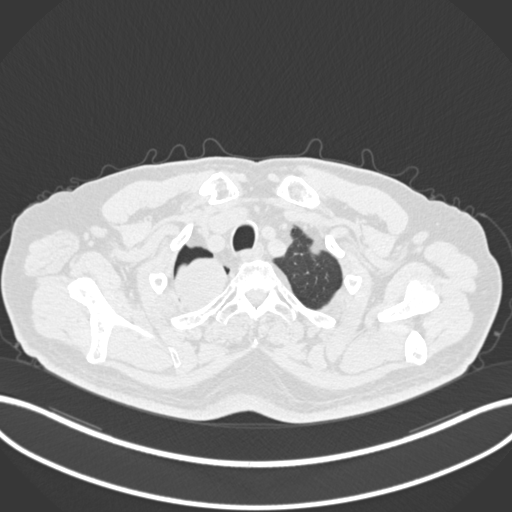
Chest CT, one axial slice. Slice 195 of 218 in the series (ordered by position). Reconstruction kernel B30f. 120 kVp. Lung window (W 1500 / L -600 HU). 512 × 512 image matrix, field of view 400 × 400 mm. Patient: male, 68 years. Case-level facts recorded for this patient, not image findings: clinical TNM (as recorded): T2a N0 M0.
Annotated regions visible in this slice (bounding box drawn by a radiologist):
- lung tumour (recorded histology: adenocarcinoma): bounding box [x1, y1, x2, y2] px = [169, 254, 233, 308]